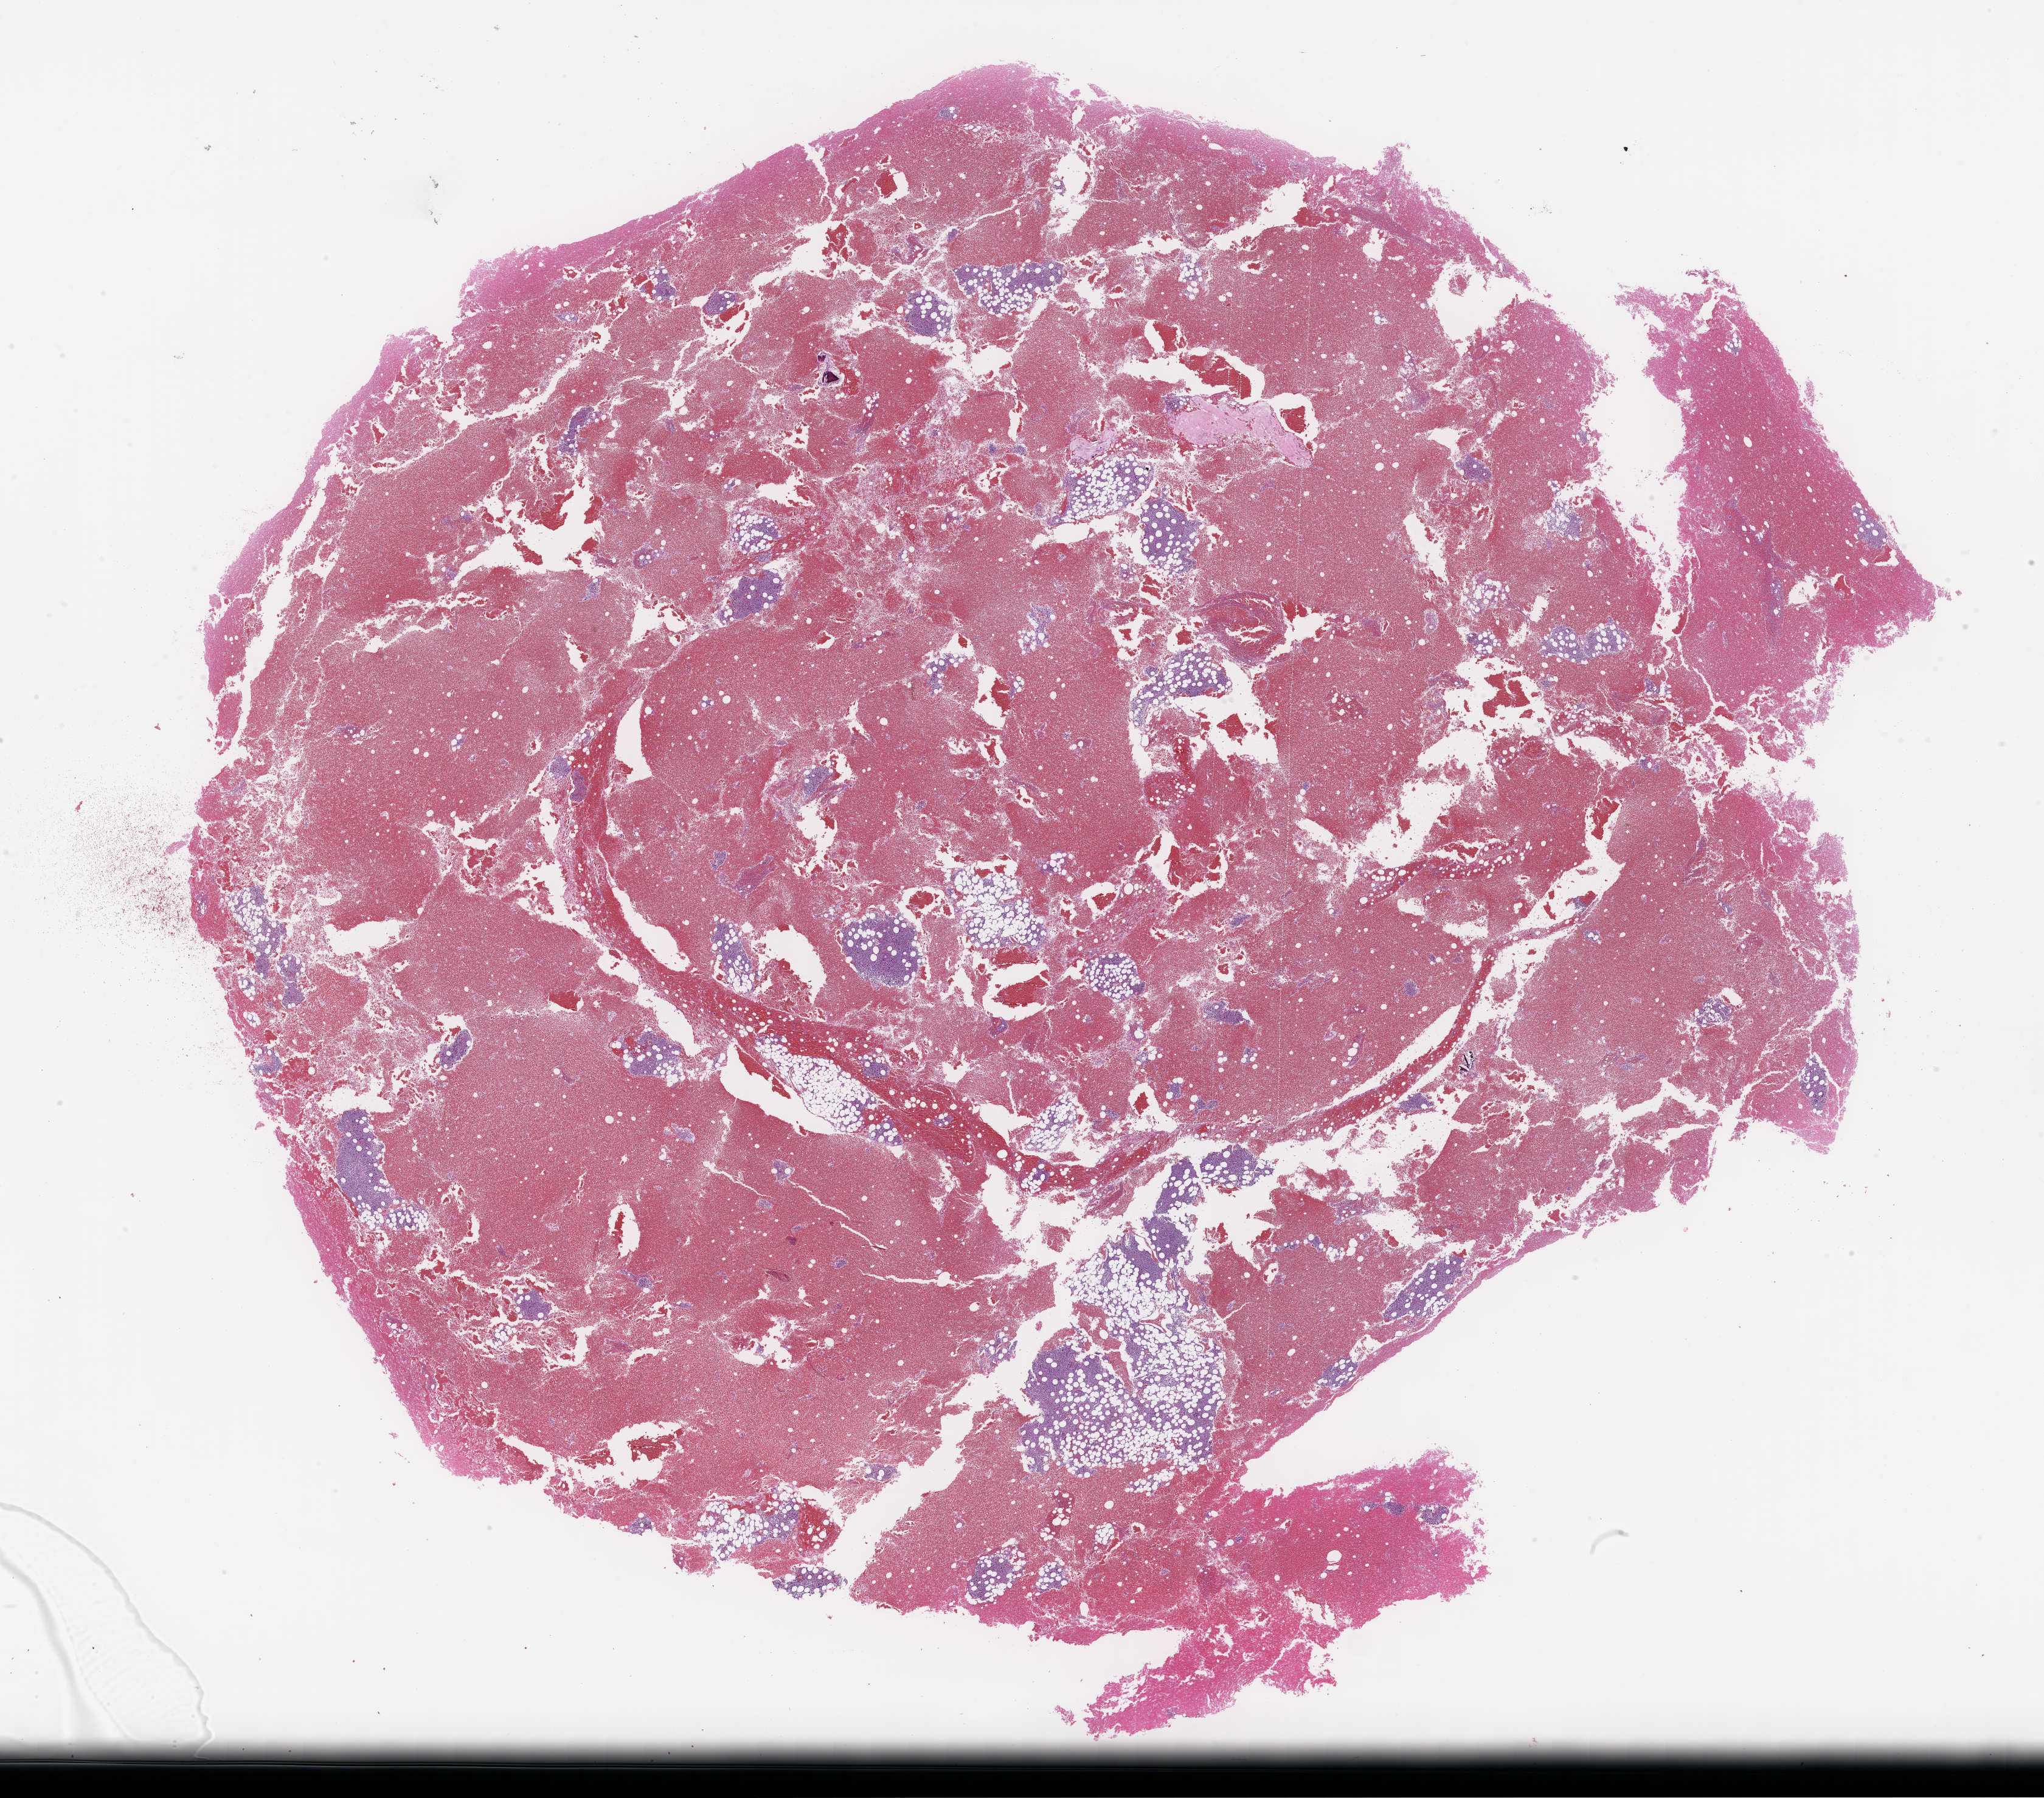
Whole-slide image, H&E stain, whole scanned area (about 27.1 x 23.9 mm) shown as a low-resolution overview. FFPE section. Tissue site: bone marrow. Archival tissue. Patient sex: male.
This section: primary tumor. Diagnosis: Plasma Cell Myeloma.